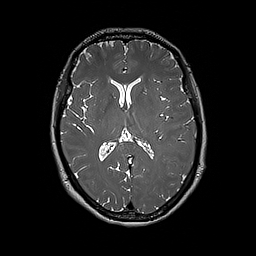
Brain MRI from a brain-tumour surgery series, one axial slice. Slice 98 of 192 in the series (ordered by position). 256 × 256 image matrix, field of view 250 × 250 mm. From the clinical record (not read from this slice): histopathology: Glioblastoma; WHO grade: 4; IDH mutation: no; tumour location: Left Frontal.
Structures marked on this image (outlined manually by an expert reader):
- tumour: bounding box <182,162,190,168> (left, top, right, bottom; pixels)